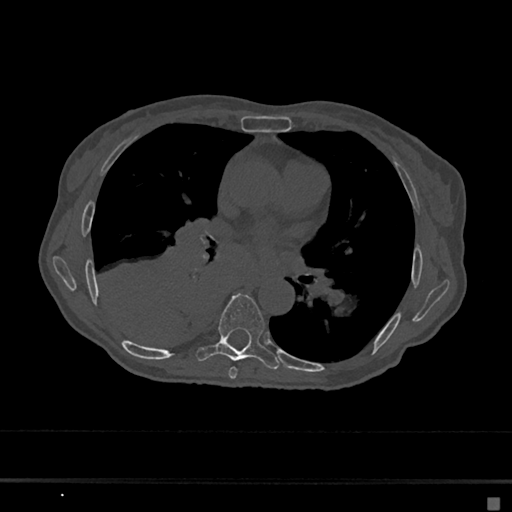
CT including the spine, one axial slice. Slice 378 of 797 in the series (ordered by position). Reconstruction kernel Br40s/3. 120 kVp. Bone window (W 1800 / L 400 HU). 0.5 mm slice thickness. 512 × 512 image matrix. Patient: female, 68 years. From the clinical record (not read from this slice): primary cancer: renal.
Structures marked on this image (semi-automatically segmented with operator editing):
- T6 vertebra: bounding box (x1, y1, x2, y2) in pixels: (228, 367, 237, 379)
- T7 vertebra: (196, 293, 280, 370)